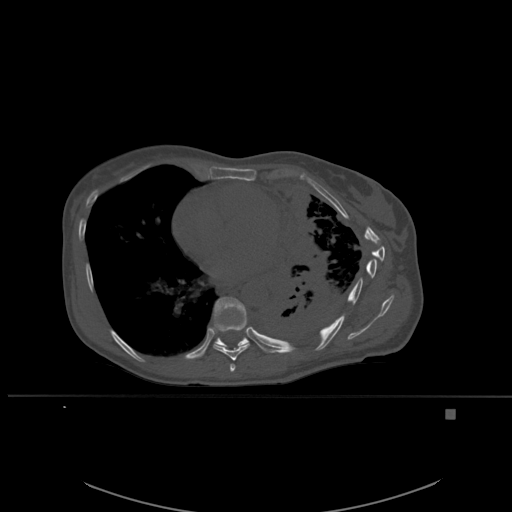
CT including the spine, one axial slice. Slice 345 of 537 in the series (ordered by position). Bone window (W 1800 / L 400 HU). 1.5 mm slice thickness. 512 × 512 image matrix, field of view 440 × 440 mm. Female patient, age 45 years. Case-level facts recorded for this patient, not image findings: primary cancer: lung.
Outlined on this slice (semi-automatic segmentation, software-assisted and operator-edited):
- T7 vertebra: box from (x=230, y=364) to (x=236, y=372) px
- T8 vertebra: (x=213, y=318)–(x=250, y=361)
- T9 vertebra: (x=213, y=297)–(x=249, y=349)